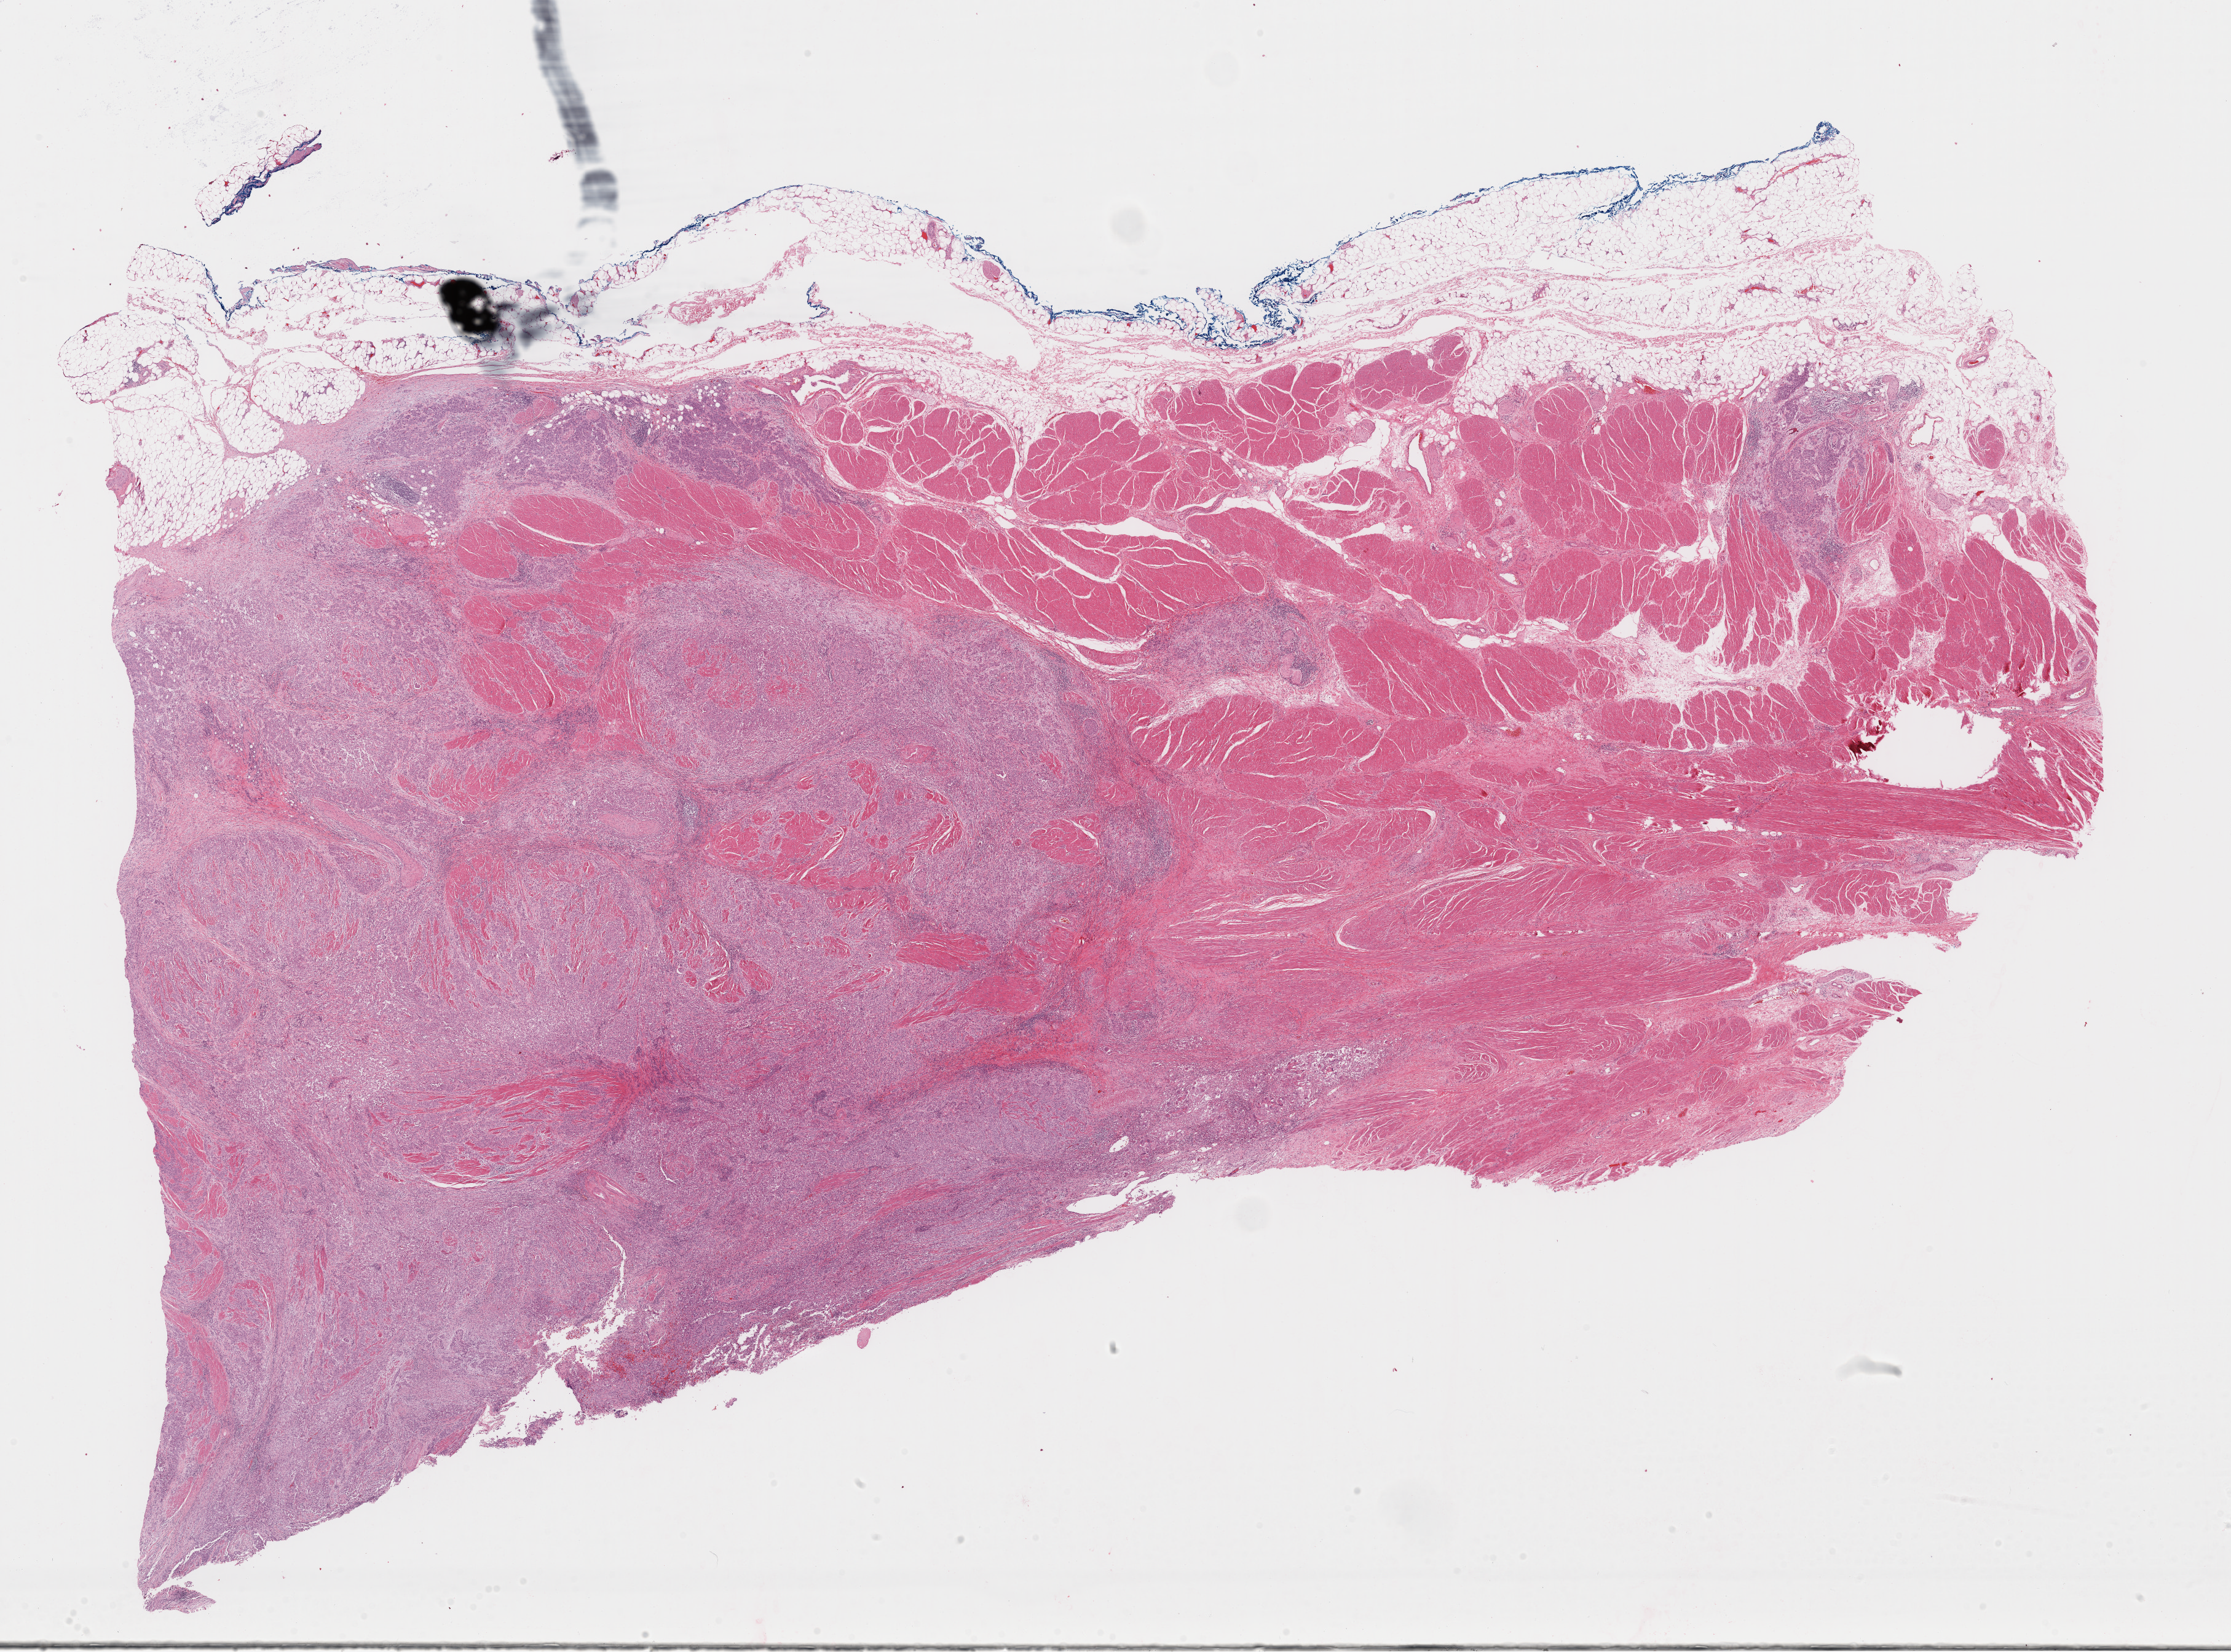
Hematoxylin and eosin (H&E) stained whole-slide image, low-resolution overview of the scanned area, about 28.7 x 21.2 mm (acquisition: 40x scan), formalin-fixed paraffin-embedded (FFPE) diagnostic section, bladder, primary tumour sample. Patient: male, age at initial diagnosis 73 years. Histologic grade: high grade.
Diagnosis: Transitional cell carcinoma (trigone of bladder). Lymph nodes positive (case pathology): 4 of 23 examined. AJCC pathologic stage: IV.